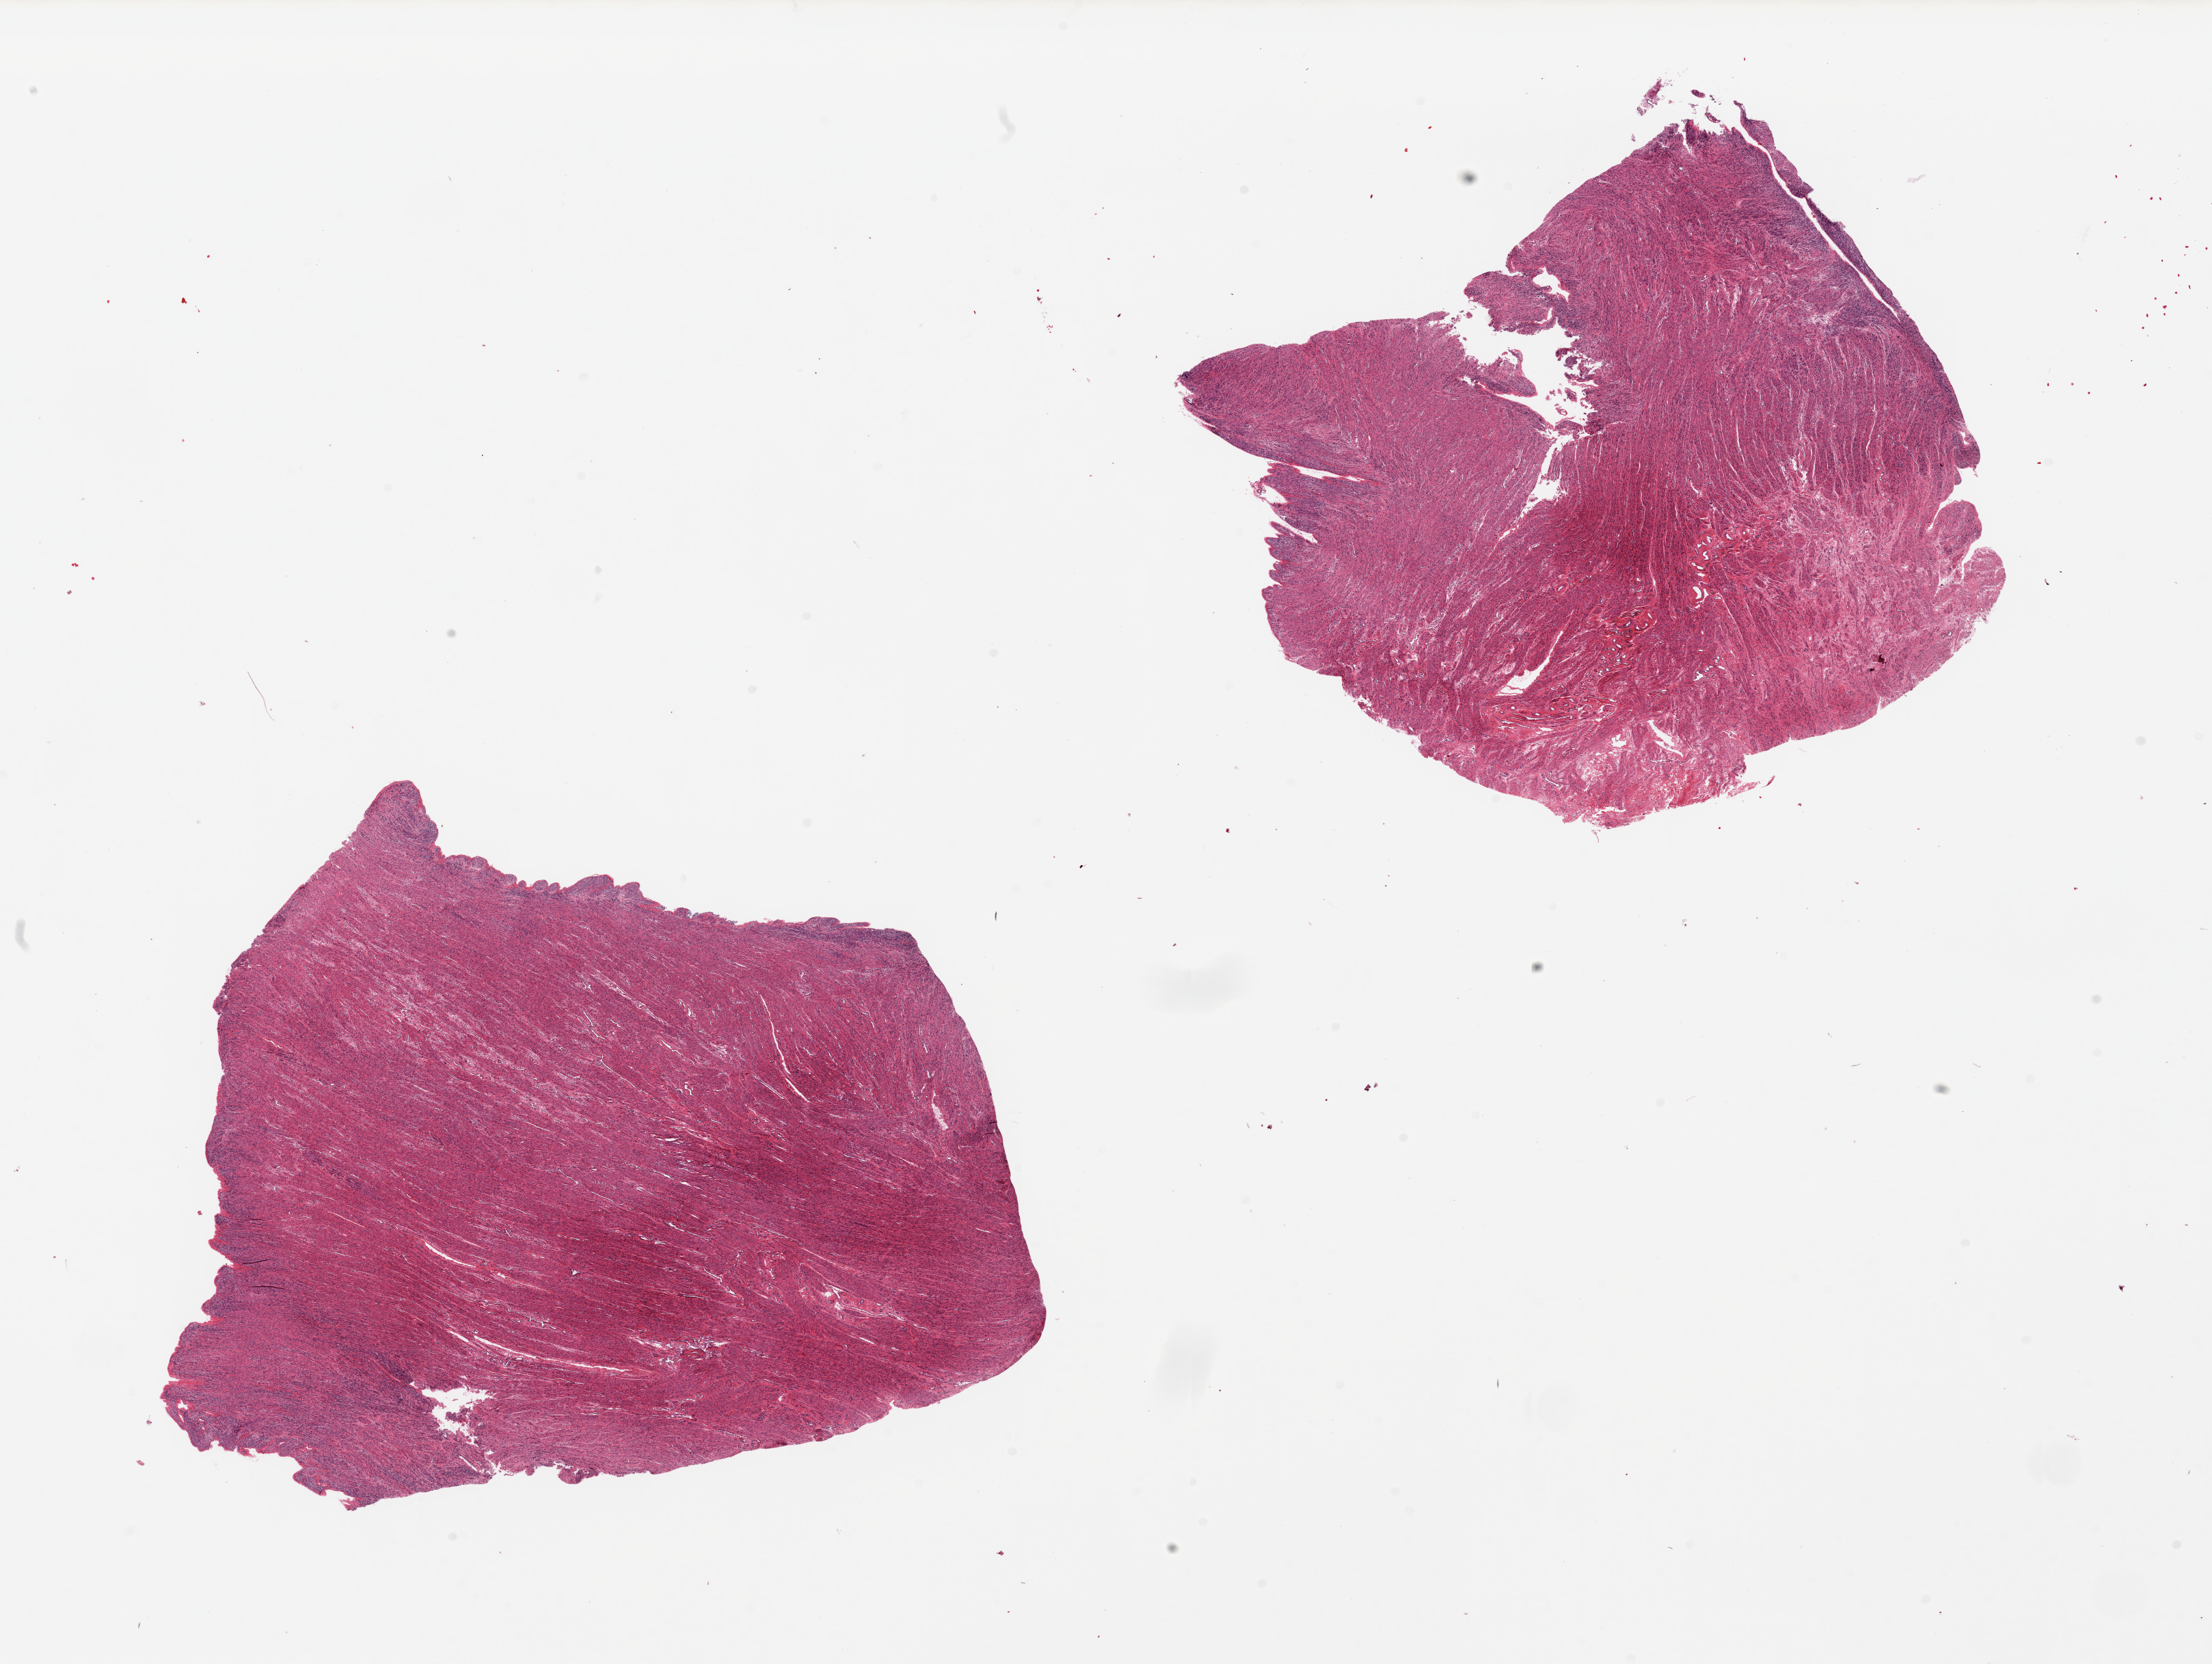
H&E whole-slide image, brightfield, low-resolution overview of the scanned area, about 25.6 x 19.3 mm. PAXgene-fixed, paraffin-embedded tissue. Target tissue: uterus. Donor tissue sample.
Reviewer comment on this tissue sample: 2 pieces, all myometrium, no significant endometrial components noted.